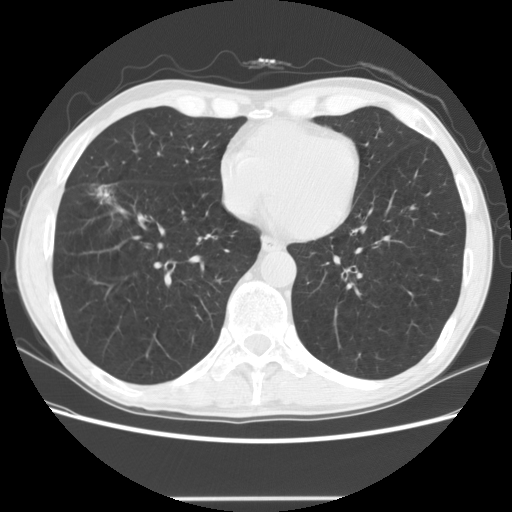
Low-dose screening chest CT, one axial slice; slice 55 of 145 in the series (ordered by position); reconstruction kernel STANDARD; 140 kVp; lung window (W 1500 / L -600 HU); 512 × 512 image matrix.
Annotated regions visible in this slice (outlined manually by an expert reader):
- lesion 1 (tumor, middle lobe of right lung): bounding box [x1, y1, x2, y2] px = [97, 185, 111, 204]